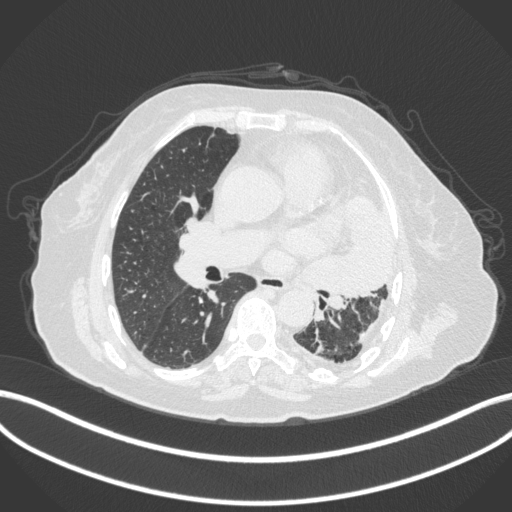
Chest CT, one axial slice. Reconstruction kernel B31f. Lung window (W 1500 / L -600 HU). 512 × 512 image matrix, field of view 400 × 400 mm. Patient: female, 75 years. From the clinical record (not read from this slice): clinical TNM (as recorded): T3 N3 M1.
Outlined on this slice (bounding box drawn by a radiologist):
- lung tumour (recorded histology: adenocarcinoma): bounding box <315,195,396,300> (left, top, right, bottom; pixels)